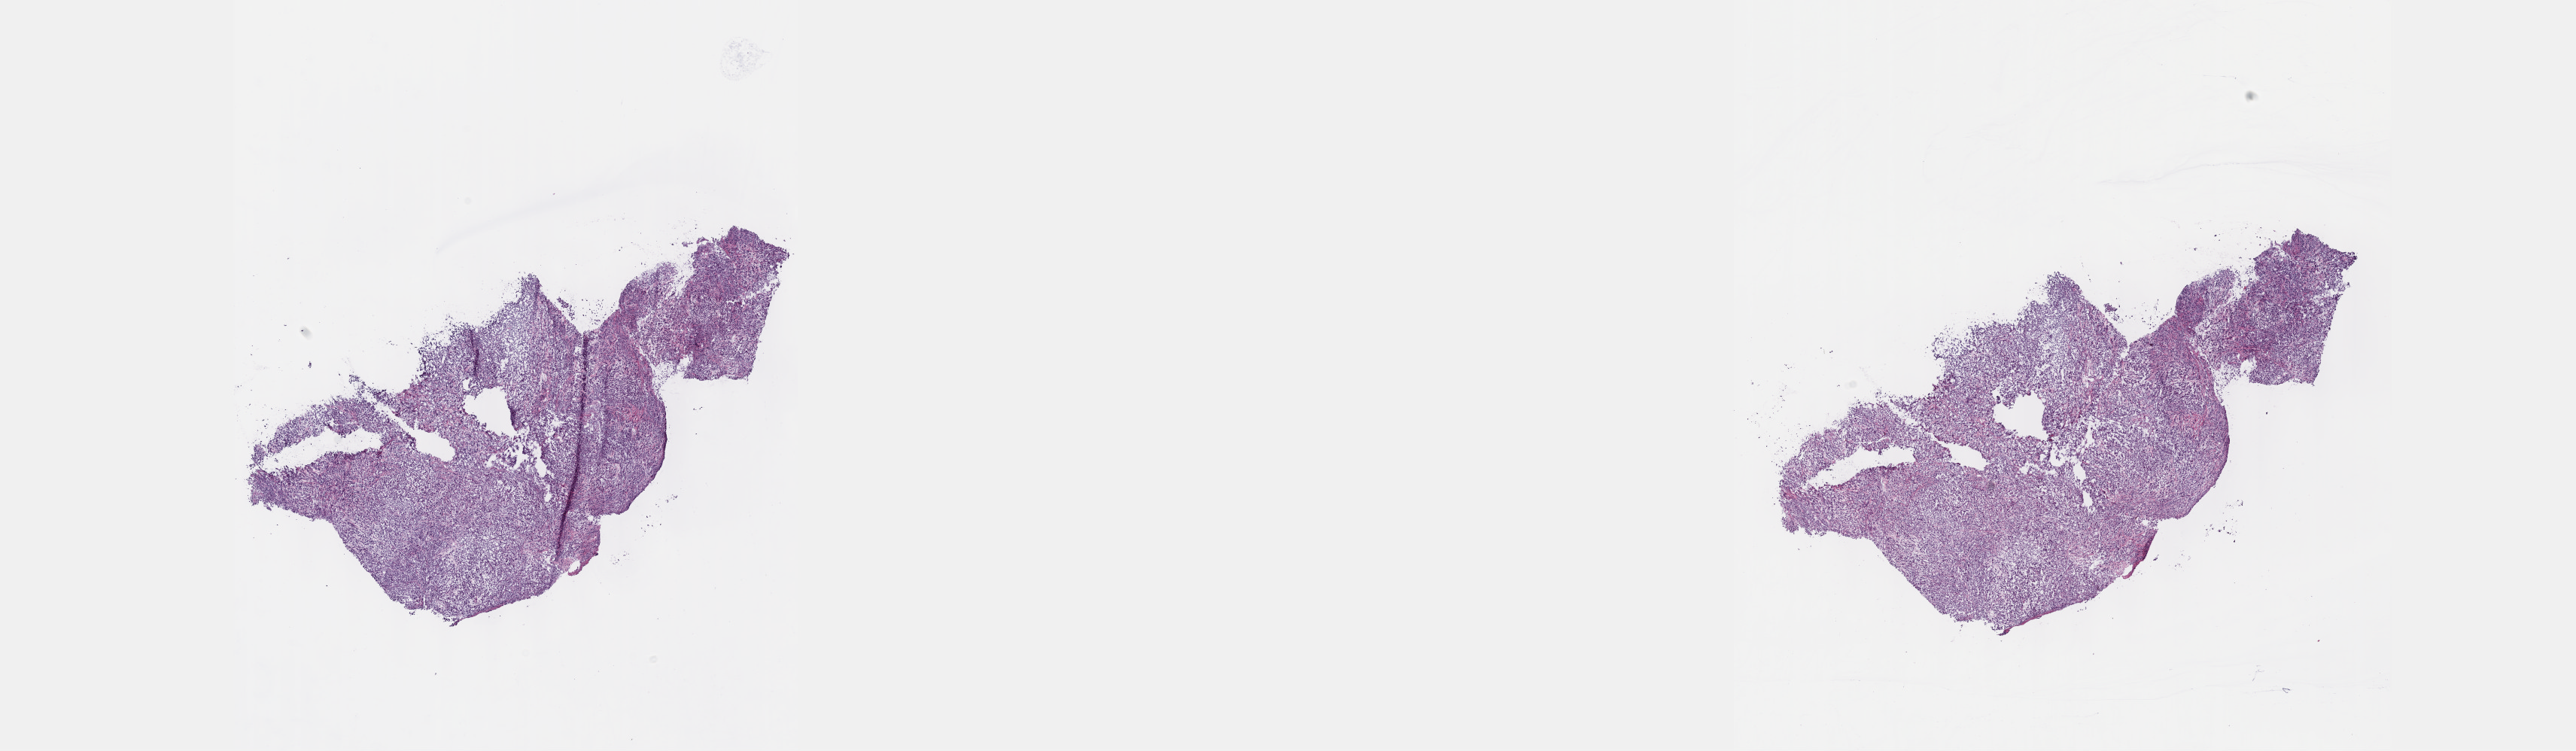
Digitized Hematoxylin and eosin (H&E) stained tissue section (whole slide) — a low-resolution overview of the entire scanned area, about 27.7 x 8.1 mm (from a 40x scan). Frozen section. Sample: primary tumour, mesothelium. Male patient; age at initial diagnosis 74 years. Composition of this section per pathologist review: tumour cells 85%, tumour nuclei 85%, normal cells 0%, stromal cells 15%, necrosis 0%. Inflammatory infiltration, as recorded: lymphocyte infiltration 3%, monocyte infiltration 1%, neutrophil infiltration 4%.
* AJCC pathologic stage: I (7th edition)
* pathologic diagnosis: Epithelioid mesothelioma, malignant (pleura, NOS)
* TNM: T1 N0 M0